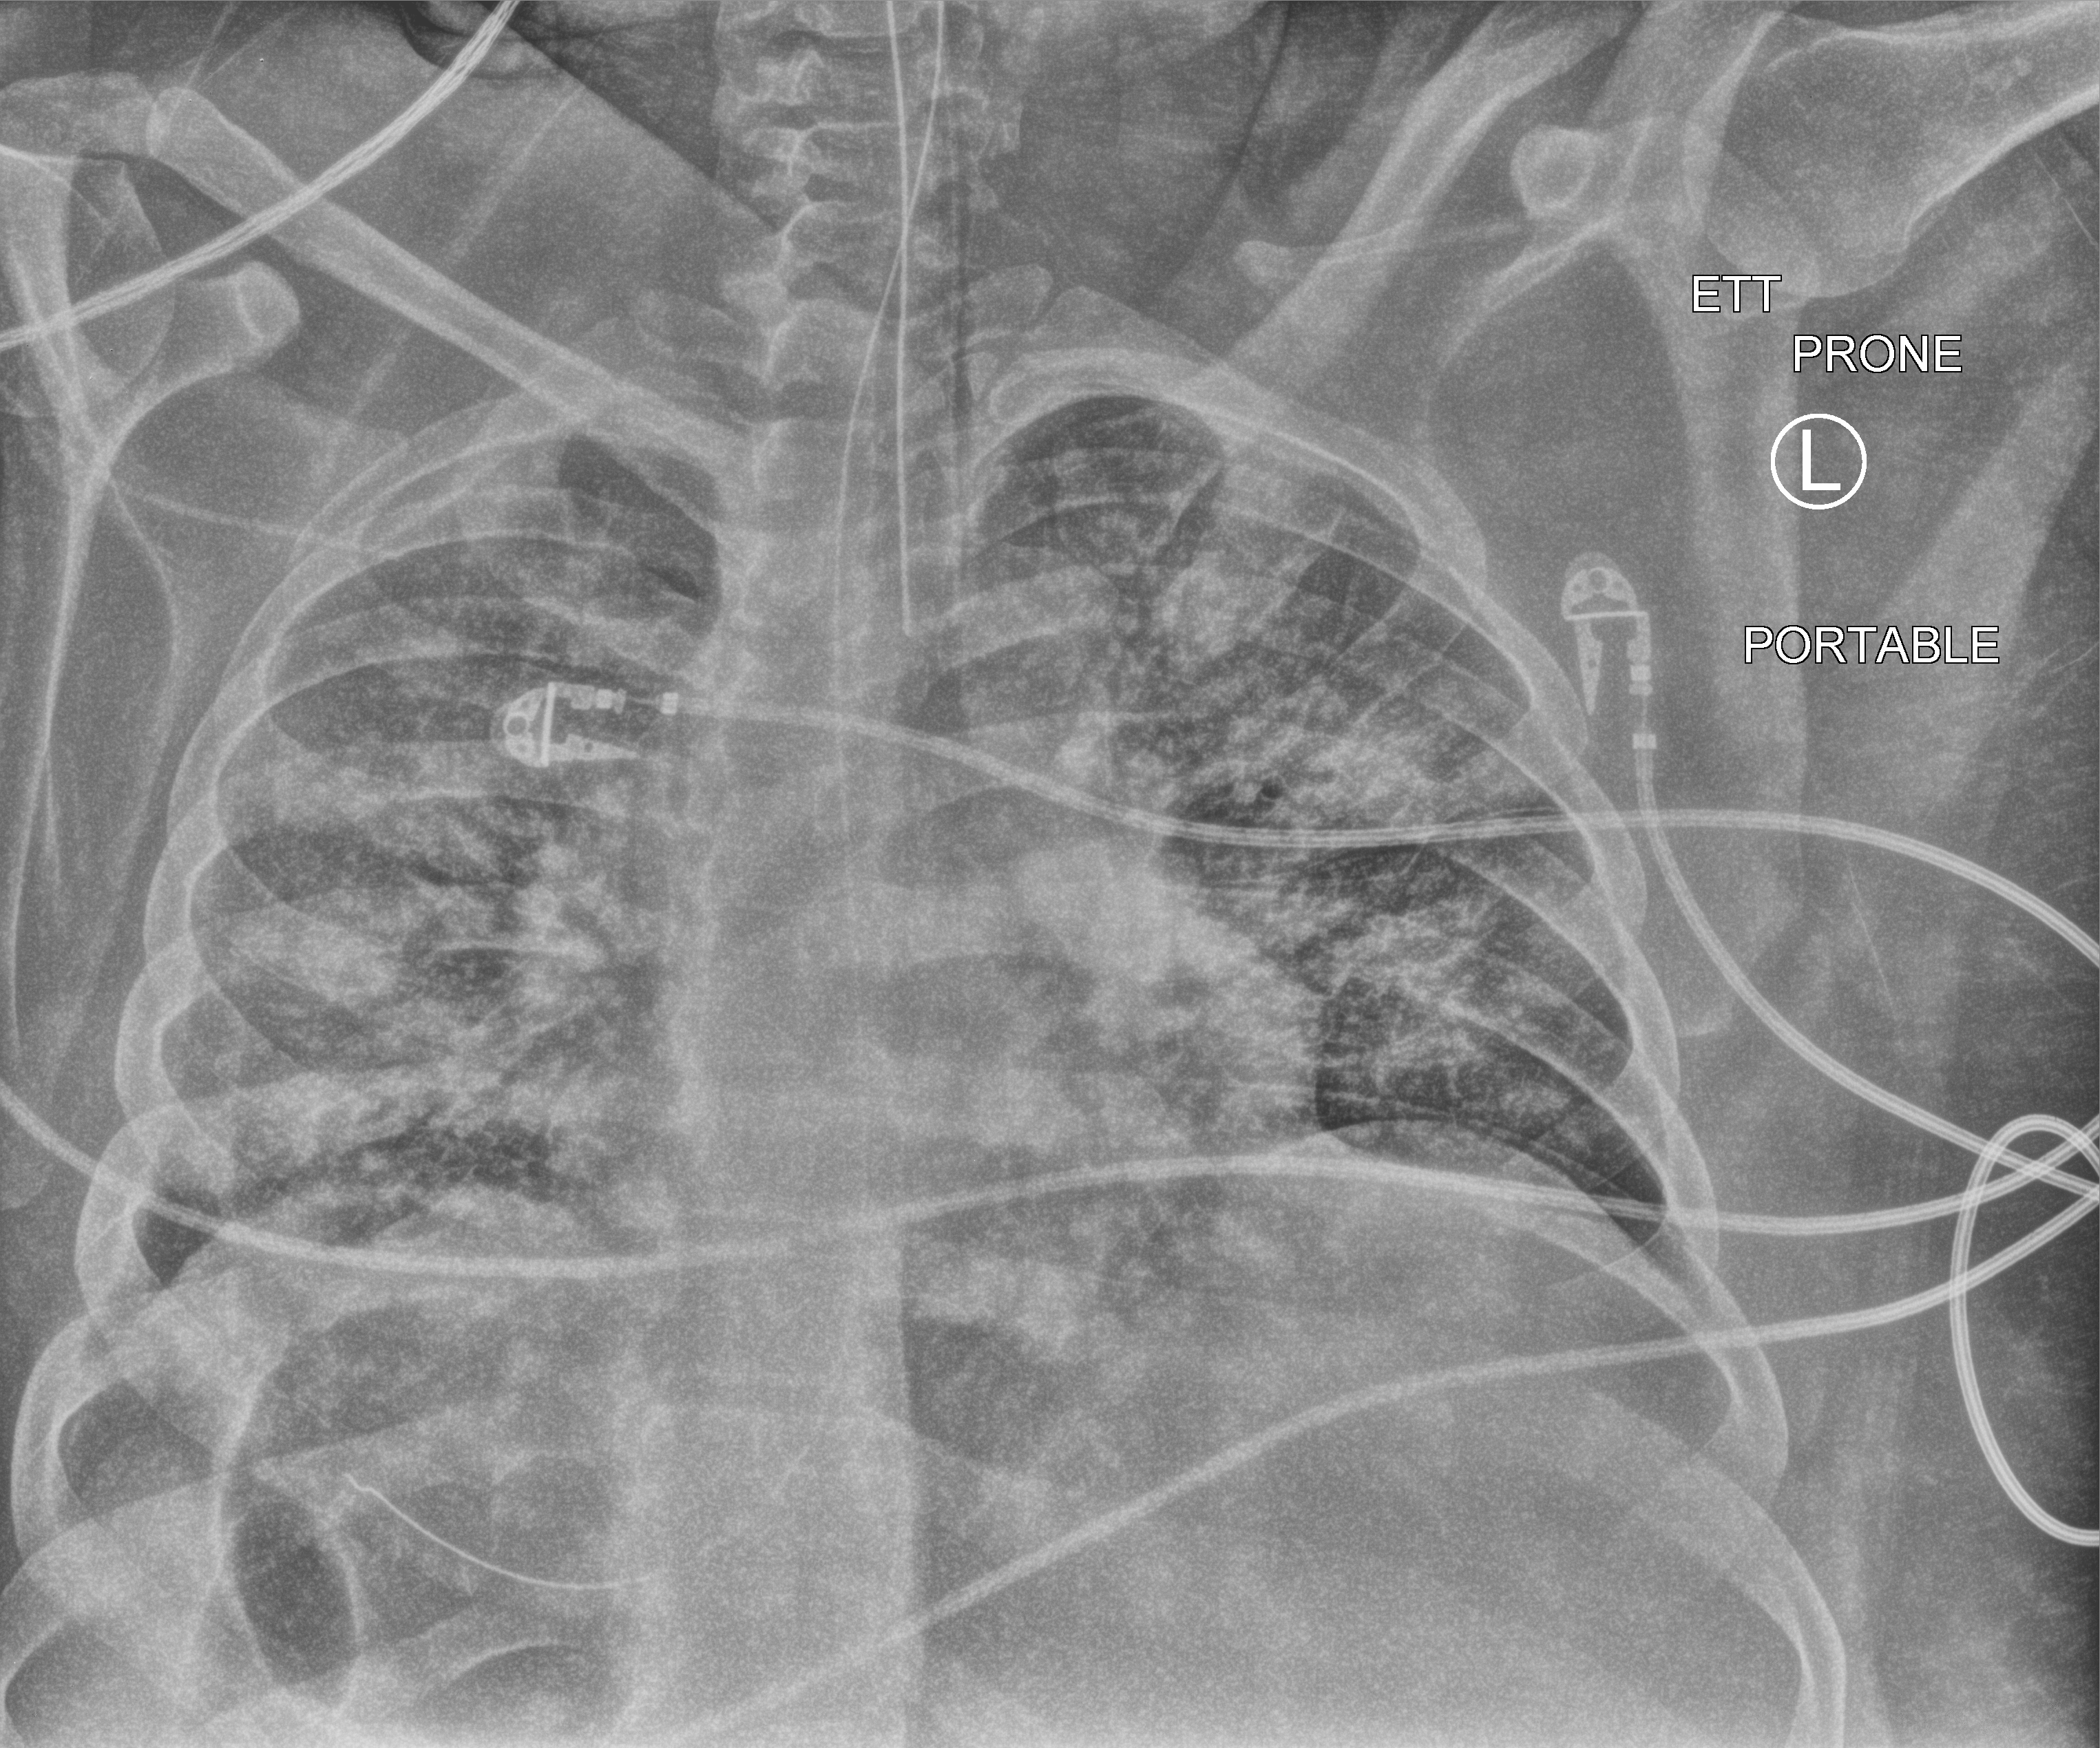
Portable chest radiograph, anteroposterior (AP) projection. Patient hospitalised with COVID-19, aged 18–59 years.
From the hospital-stay record, not from the radiograph (when in the stay this image was taken is not recorded): chronic kidney disease (admission record): no; length of hospital stay: 15 days; mechanically ventilated during this hospital stay: yes.